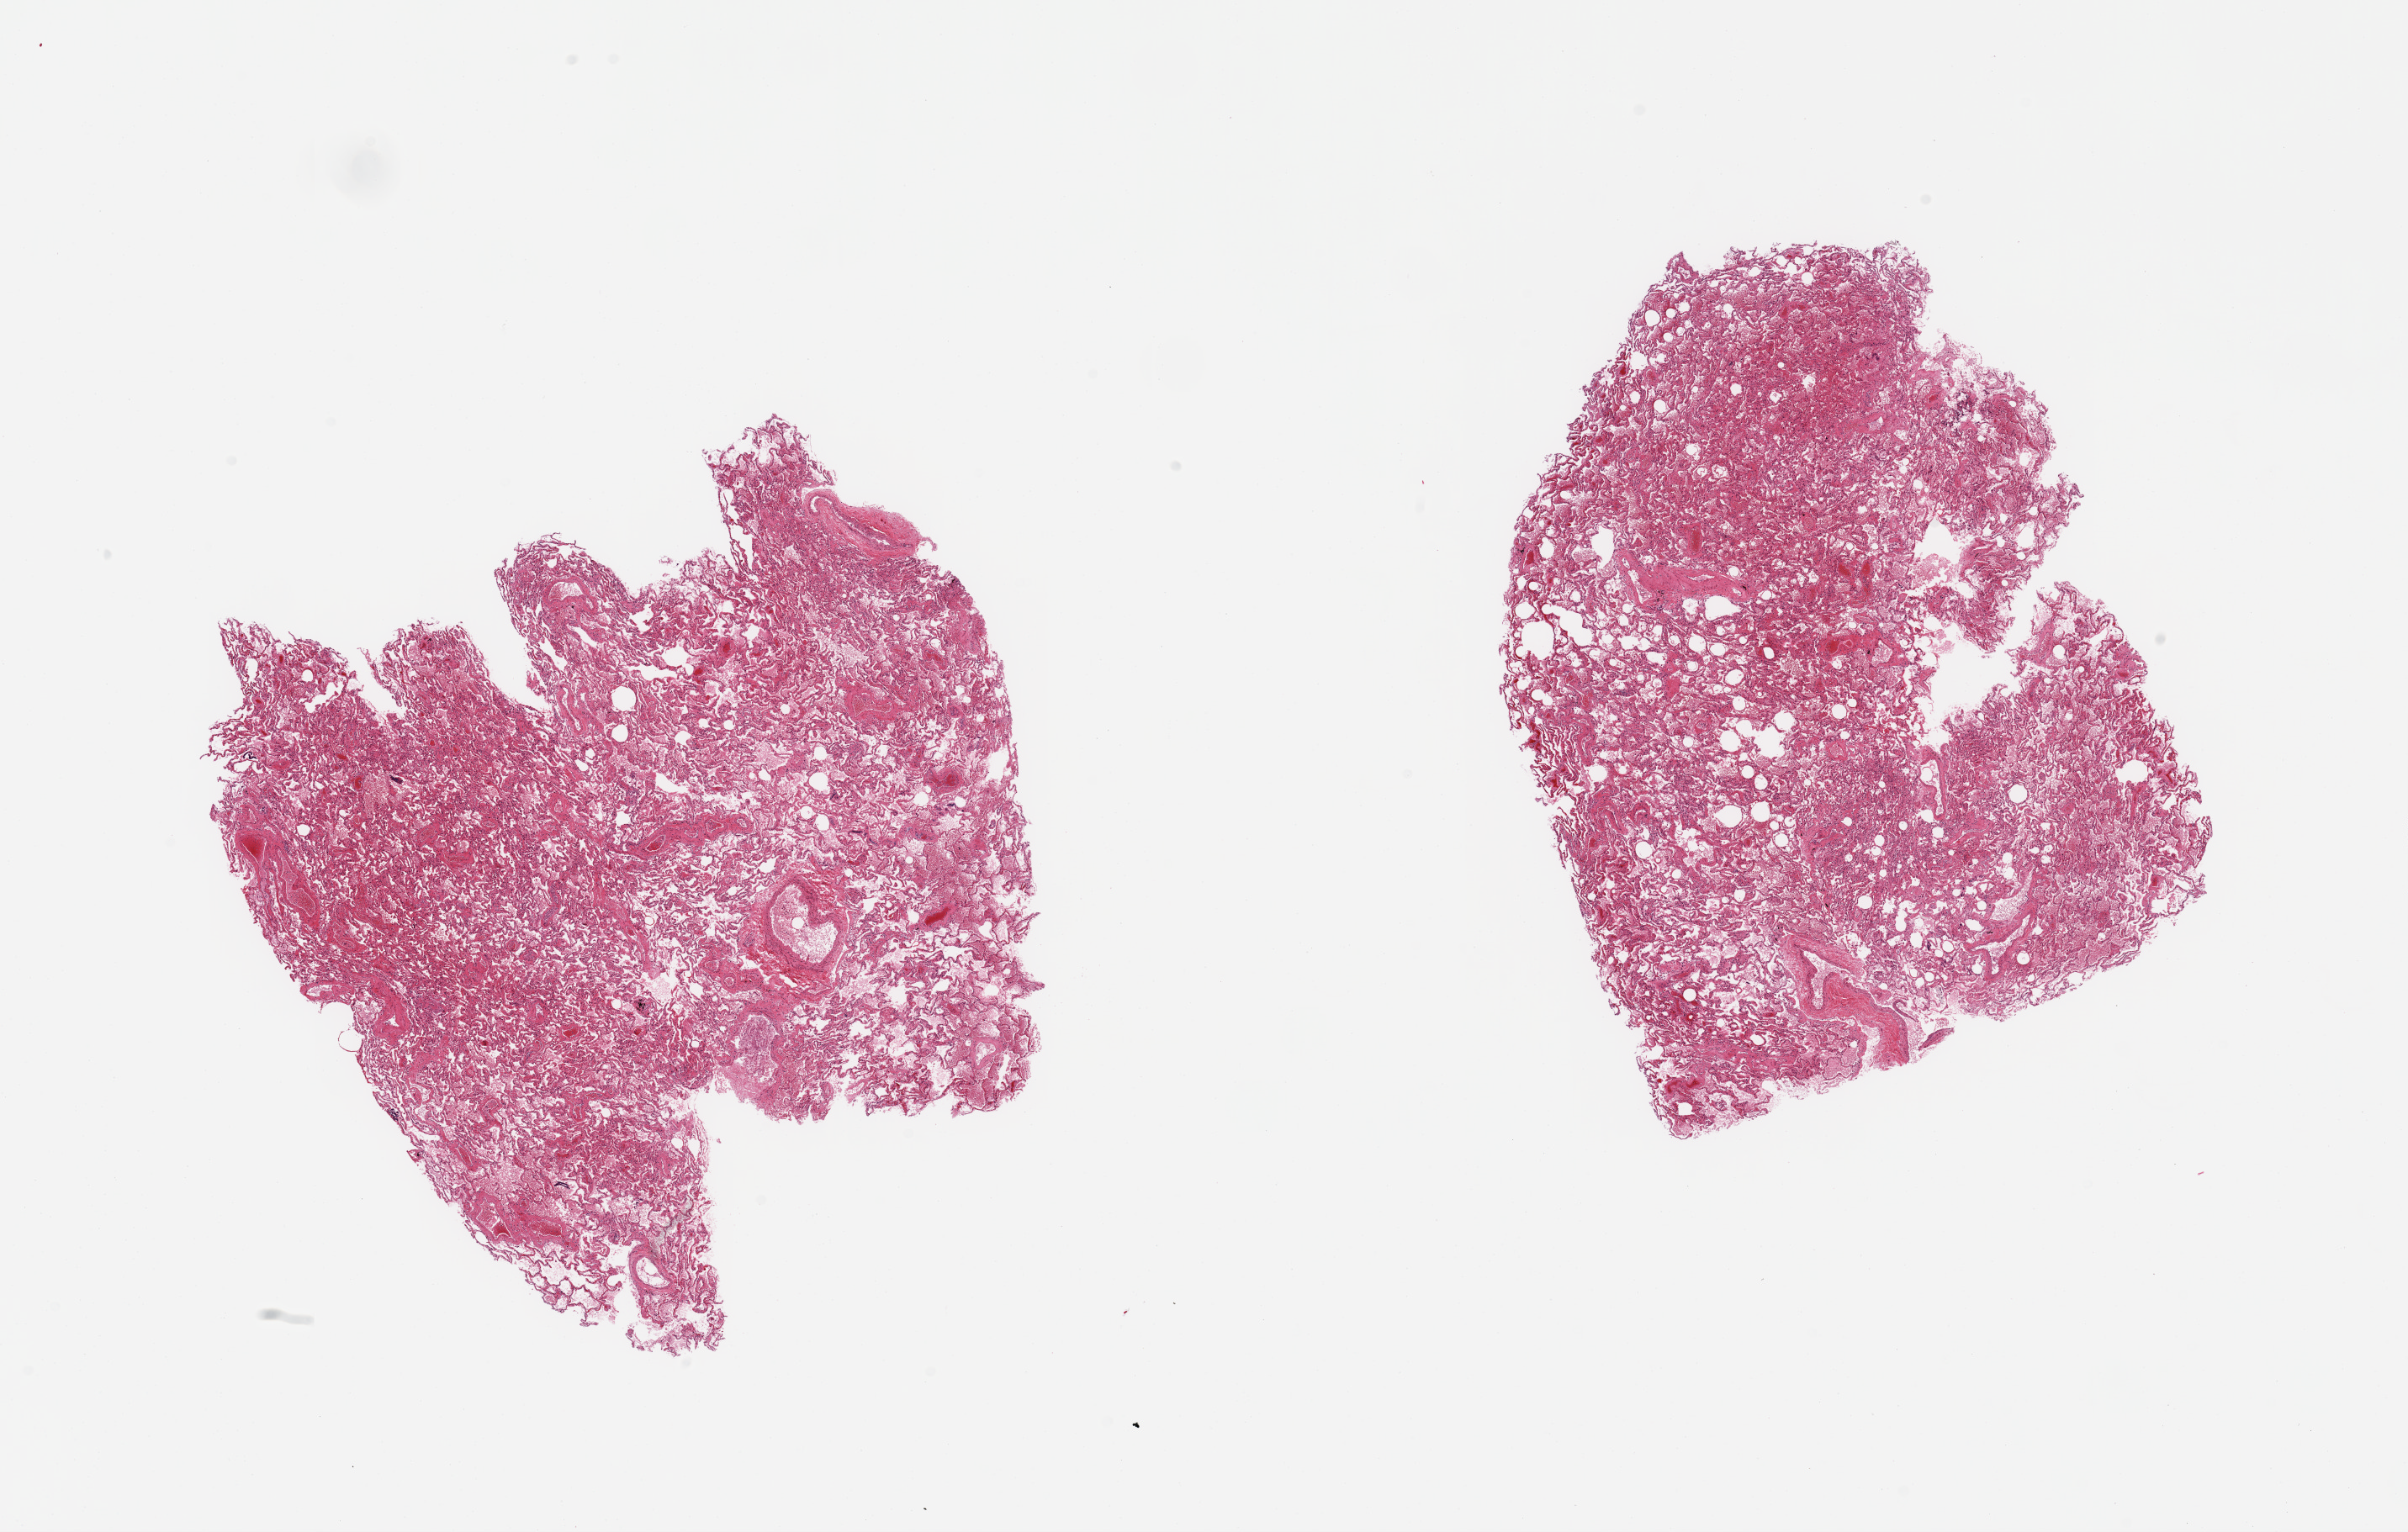
Digitized hematoxylin and eosin (H&E)-stained section, low-resolution overview of the scanned area, about 22.6 x 14.4 mm. PAXgene-fixed paraffin-embedded (PFPE) section. Target tissue: lung. Tissue donor sample. Donor: male.
Reviewer comment on this tissue sample: 2 pieces, moderate edema/atalectasis.